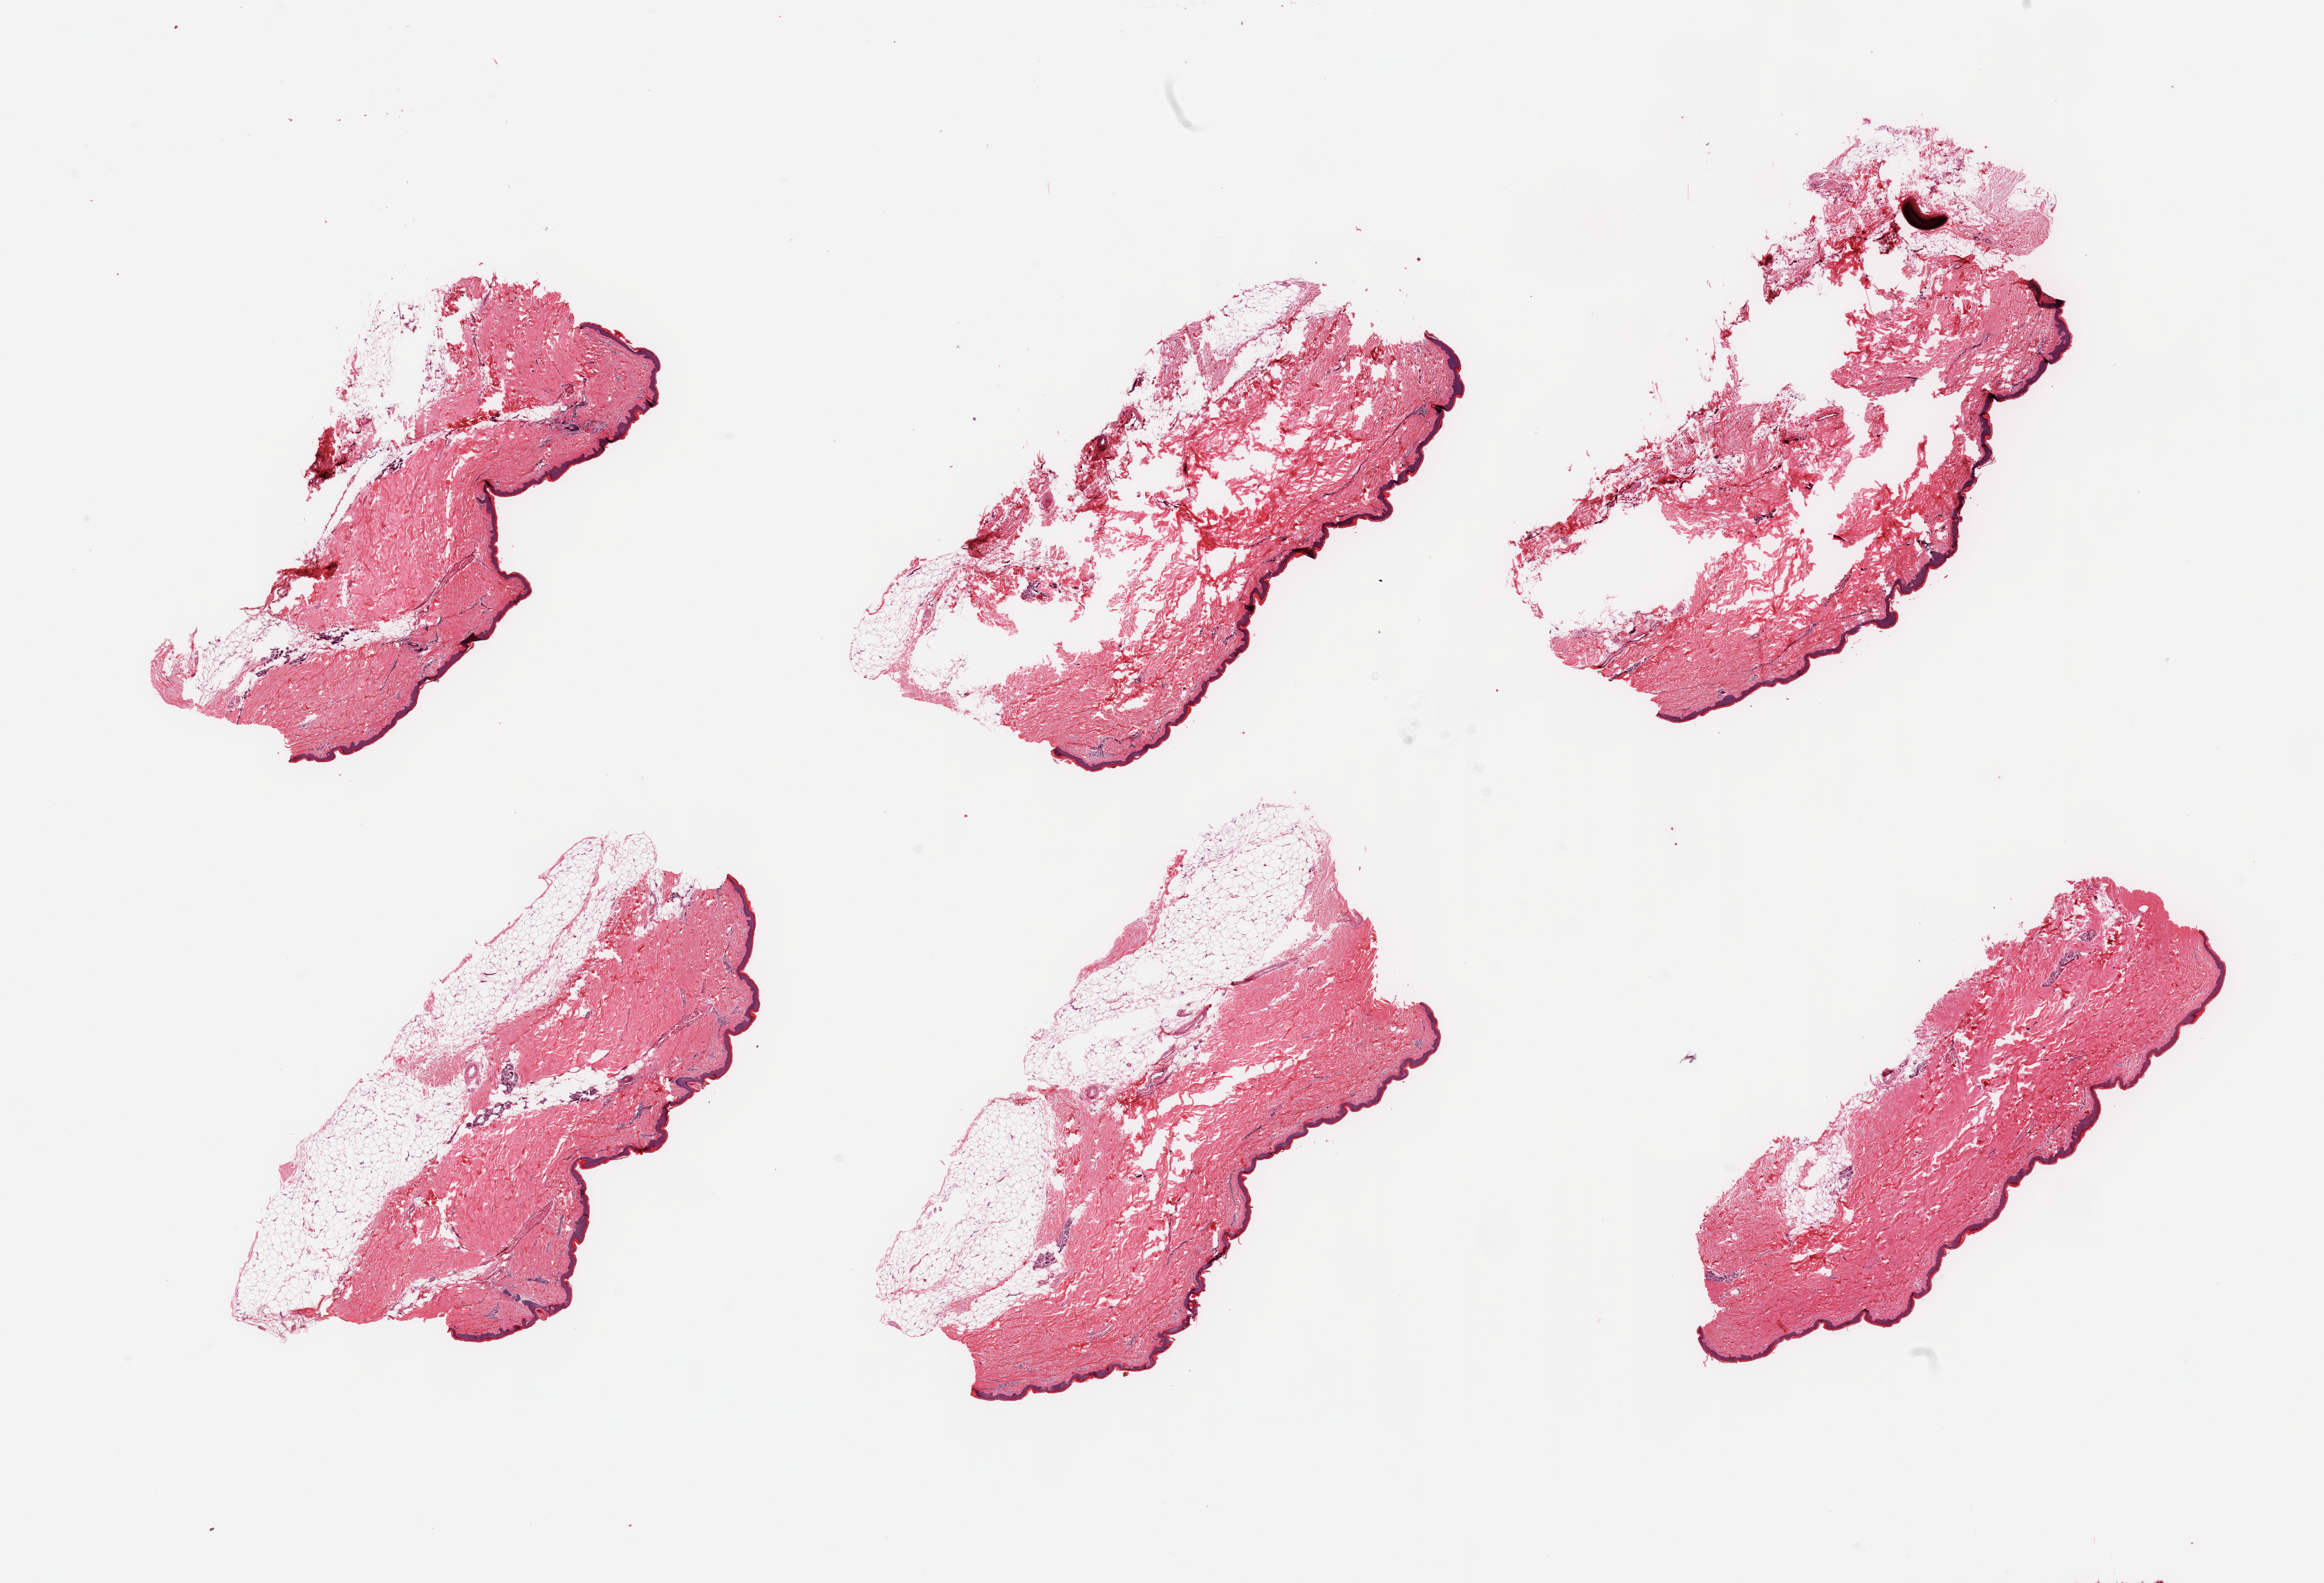
H&E whole-slide image — a low-resolution overview of the entire scanned area, about 26.6 x 18.1 mm (slide scanned at 20x); PAXgene-fixed, paraffin-embedded tissue; sampled site (target tissue): skin of lower leg; donor tissue sample. Donor: female.
* reviewer comment on this tissue sample: 6 pieces: up to 1.3 mm subcutaneous fat